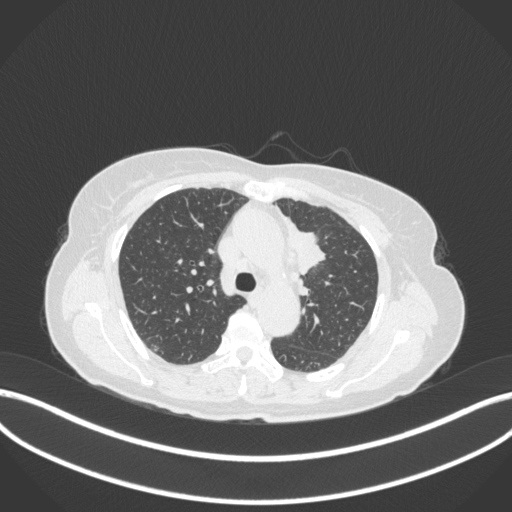
Chest CT, one axial slice; slice 233 of 368 in the series (ordered by position); 120 kVp; lung window (W 1500 / L -600 HU); 1 mm slice thickness; 512 × 512 image matrix, field of view 400 × 400 mm. Patient: female, 65 years. Case-level facts recorded for this patient, not image findings: clinical TNM (as recorded): T2a N0 M0; histopathological grade: G2-3.
Annotated regions visible in this slice (bounding box drawn by a radiologist):
- lung tumour (recorded histology: adenocarcinoma): box from (x=281, y=214) to (x=326, y=278) px